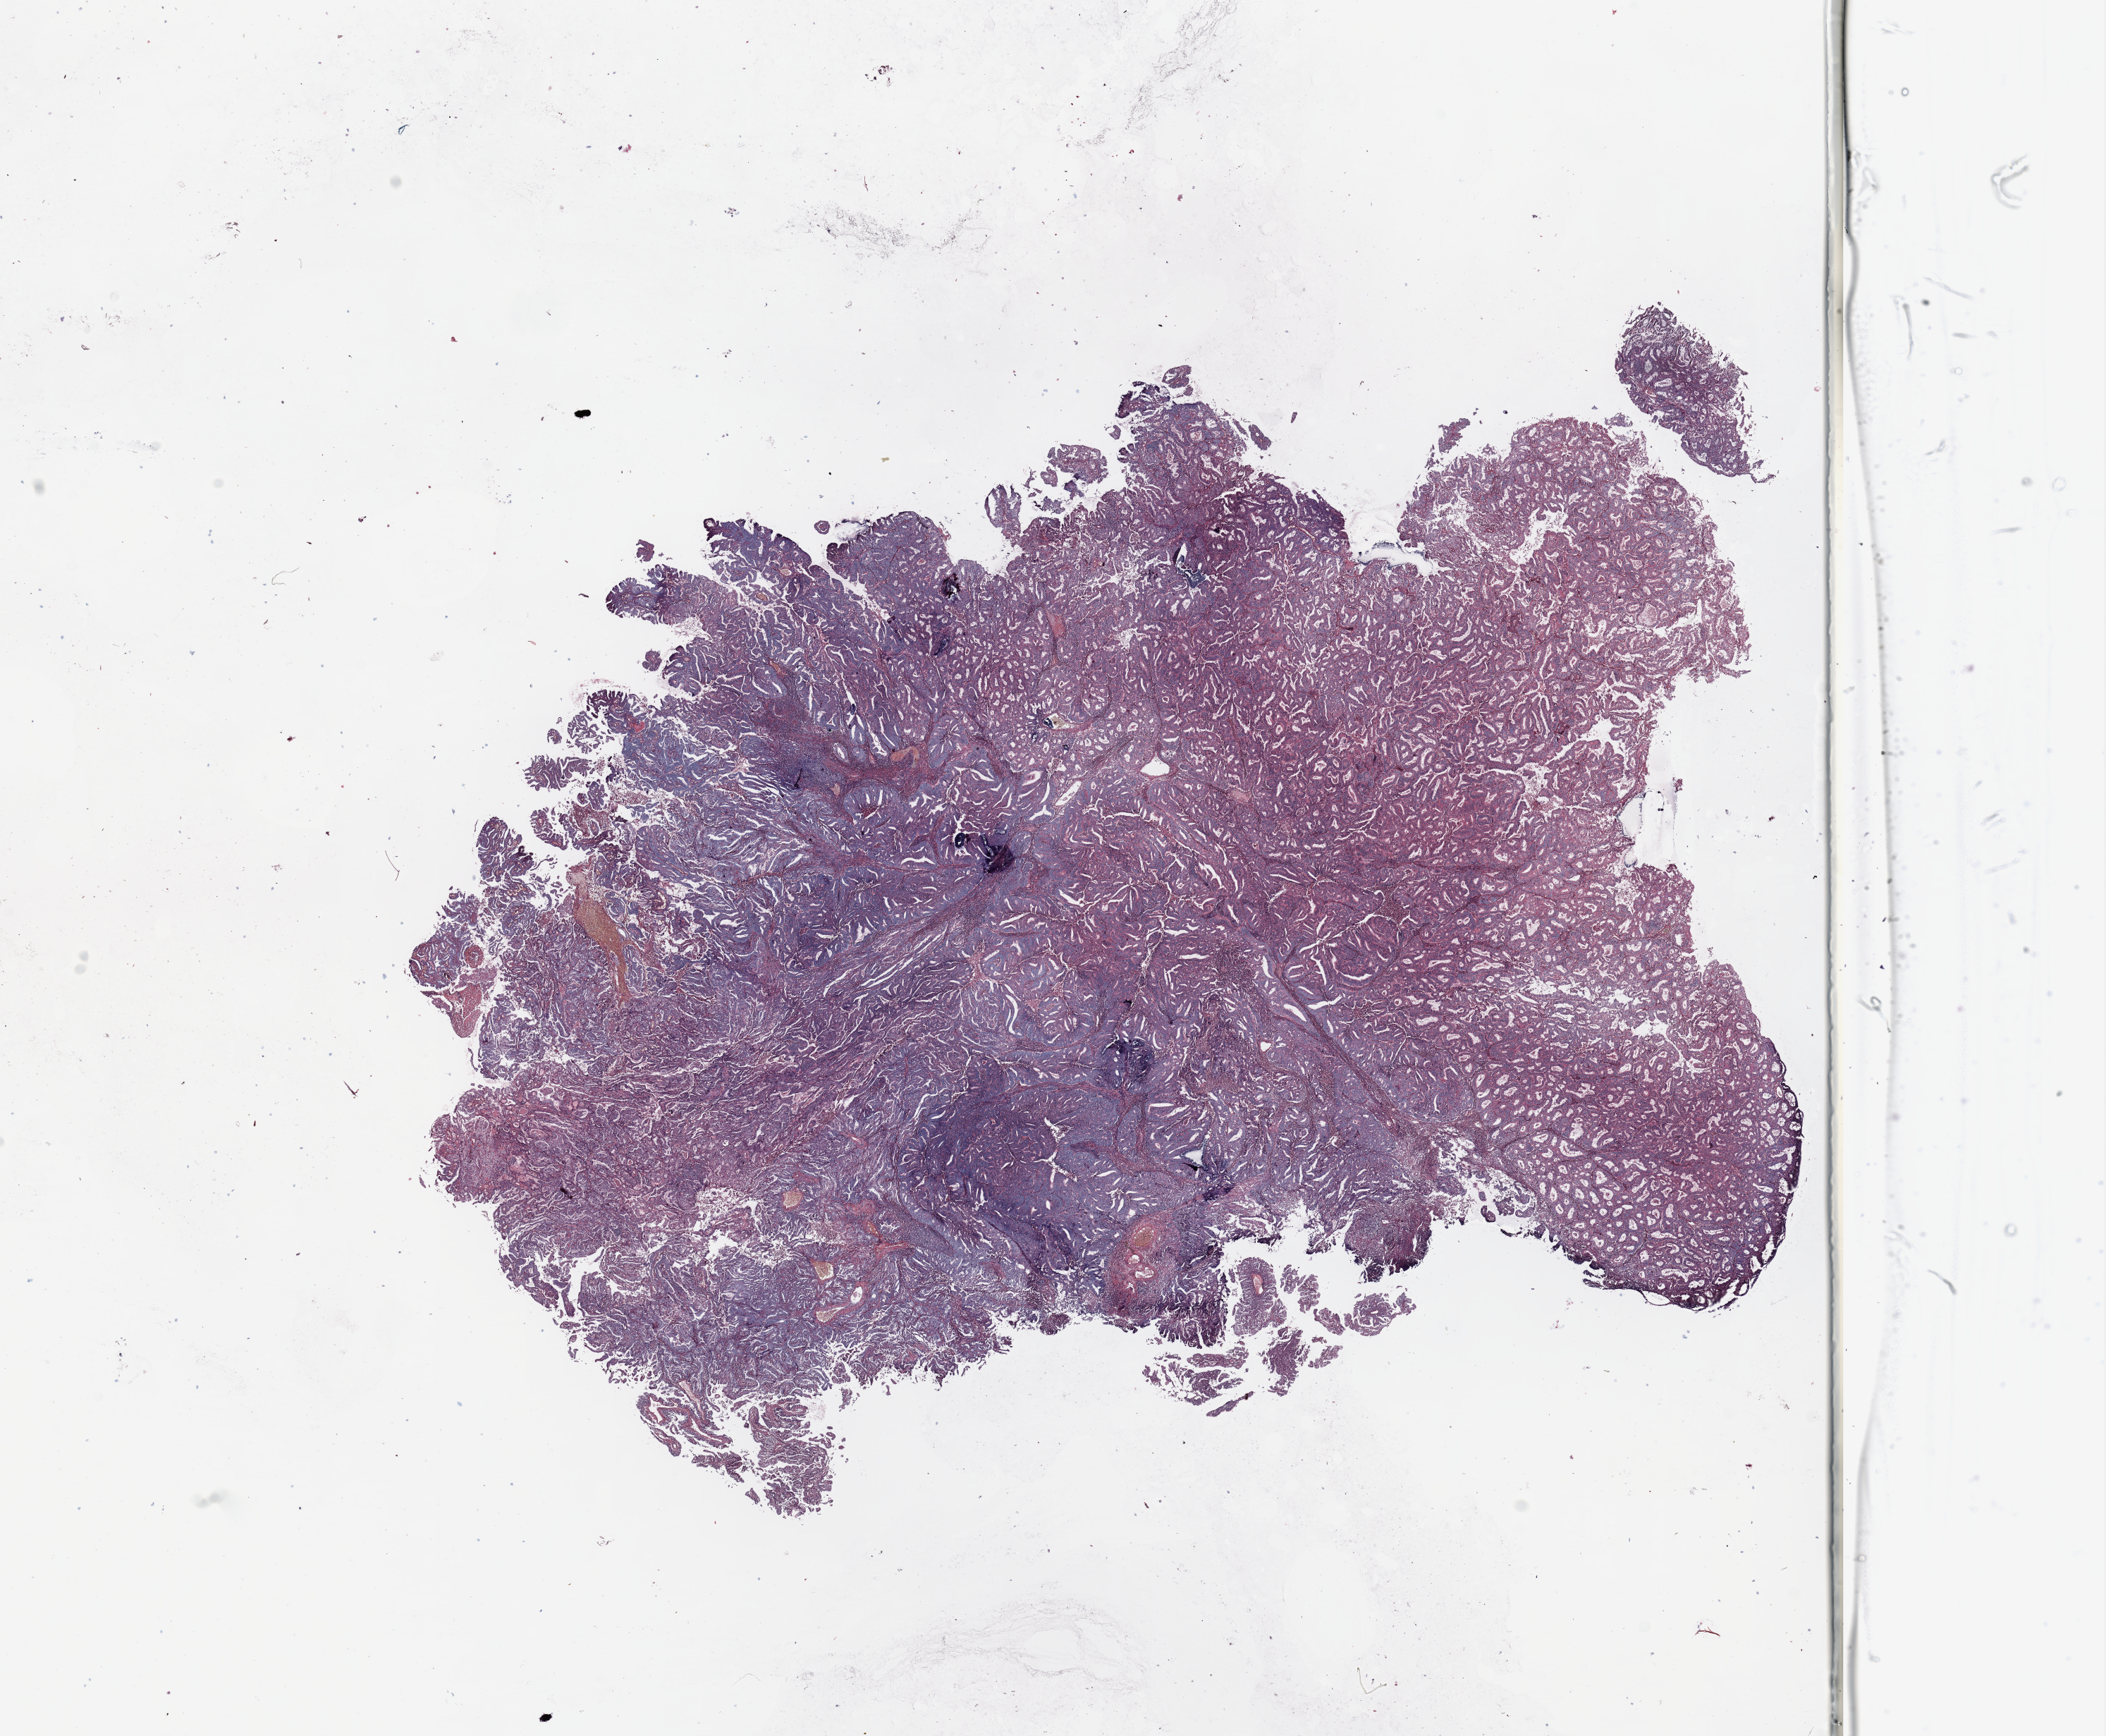
Whole-slide histology image, Hematoxylin and eosin (H&E) stained, shown as a low-resolution overview of the whole scanned area (about 23.6 x 19.5 mm, slide scanned at 20x), tumour tissue sample, uterus. Patient: female, age 63 years. Histologic grade: G2 (moderately differentiated).
Histologic diagnosis: Endometrioid adenocarcinoma, NOS. AJCC pathologic stage: III.